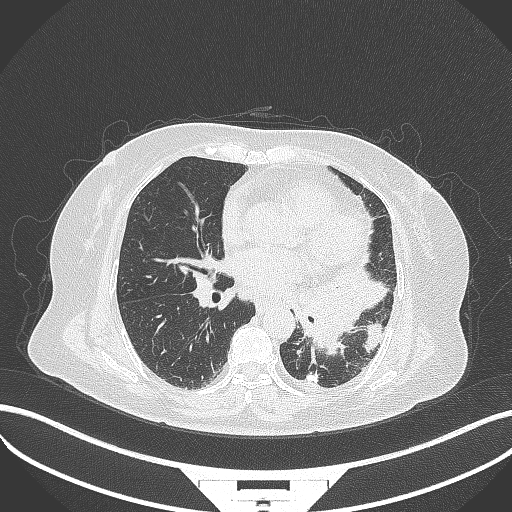
Chest CT, one axial slice; position 165 of 322 along the scan axis; 120 kVp; lung window (W 1500 / L -600 HU); 512 × 512 image matrix. Female patient, age 69 years. From the clinical record (not read from this slice): clinical TNM (as recorded): T2b N3 M1.
Structures marked on this image (bounding box drawn by a radiologist):
- lung tumour (recorded histology: adenocarcinoma): bounding box [x1, y1, x2, y2] px = [290, 265, 390, 357]